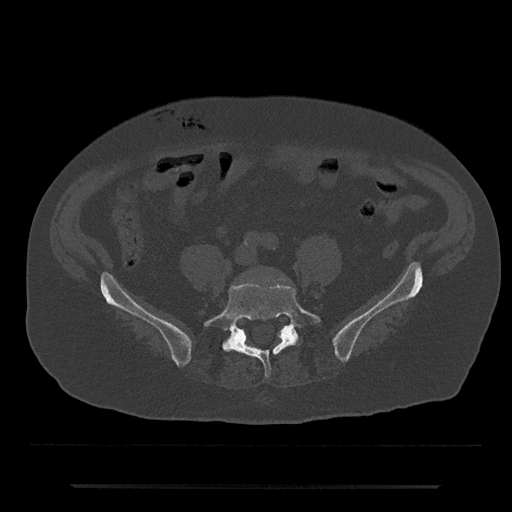
CT including the spine, one axial slice; position 289 of 797 along the scan axis; 120 kVp; bone window (W 1800 / L 400 HU); 512 × 512 image matrix, field of view 434 × 434 mm. Patient: male, 80 years. Case-level facts recorded for this patient, not image findings: primary cancer: prostate; vertebrae with lytic lesions (as recorded): L1, T11.
Annotated regions visible in this slice (semi-automatic segmentation, software-assisted and operator-edited):
- L5 vertebra: bounding box [x1, y1, x2, y2] px = [203, 283, 321, 377]